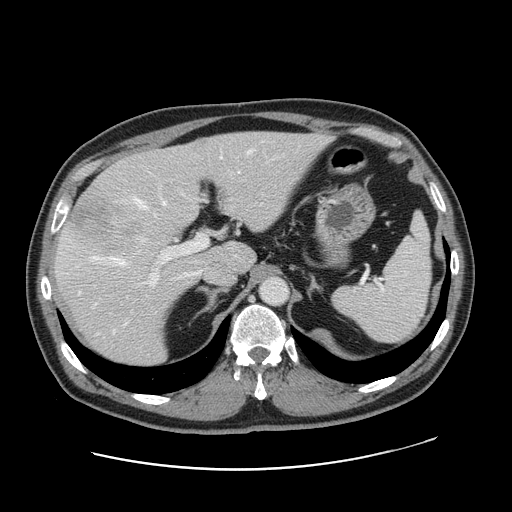
Contrast-enhanced abdominal CT, one axial slice; position 110 of 178 along the scan axis; intravenous contrast given; soft-tissue window (W 400 / L 40 HU); 2.5 mm slice thickness; 512 × 512 image matrix, field of view 403 × 403 mm. Male patient, age 63 years. Case-level facts recorded for this patient, not image findings: diagnosis: colorectal cancer liver metastases, imaged before liver resection; multiple liver metastases: yes; largest metastasis: 8 cm; disease in both lobes: yes.
Outlined on this slice (outlined manually by an expert reader):
- hepatic veins: bounding box (x1, y1, x2, y2) in pixels: (113, 150, 251, 265)
- liver: (56, 132, 326, 367)
- planned liver remnant (the part of the liver to remain after resection): (131, 132, 325, 273)
- portal vein (with intrahepatic branches): (143, 196, 223, 282)
- liver metastasis: (67, 204, 133, 258)